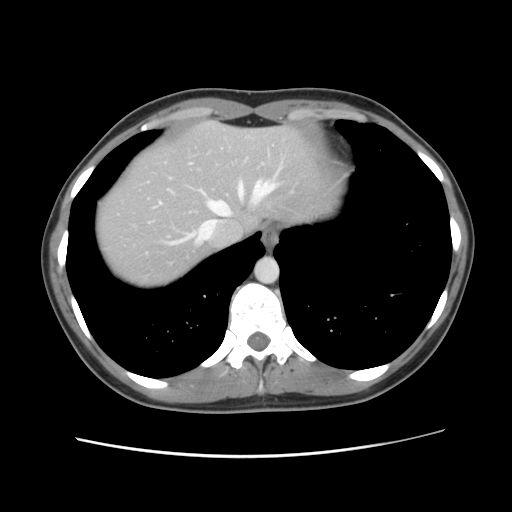
Contrast-enhanced abdominal CT, one axial slice. Soft-tissue window (W 400 / L 40 HU). 512 × 512 image matrix, field of view 339 × 339 mm. Female patient, age 33 years. Case-level facts recorded for this patient, not image findings: diagnosis: colorectal cancer liver metastases, imaged before liver resection; multiple liver metastases: yes; largest metastasis: 4.5 cm; disease in both lobes: yes.
Outlined on this slice (outlined manually by an expert reader):
- hepatic veins: bounding box <160,181,278,243> (left, top, right, bottom; pixels)
- liver: <95,122,329,289>
- planned liver remnant (the part of the liver to remain after resection): <95,122,328,289>